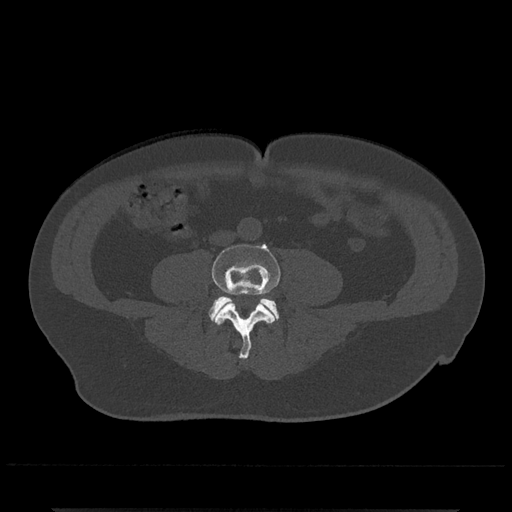
CT including the spine, one axial slice. Position 136 of 797 along the scan axis. Reconstruction kernel Br40s/3. Bone window (W 1800 / L 400 HU). 0.5 mm slice thickness. 512 × 512 image matrix. Male patient, age 67 years. From the clinical record (not read from this slice): primary cancer: prostate.
Annotated regions visible in this slice (semi-automatic segmentation, software-assisted and operator-edited):
- L4 vertebra: bounding box [x1, y1, x2, y2] px = [212, 244, 280, 359]
- L5 vertebra: [209, 296, 279, 320]